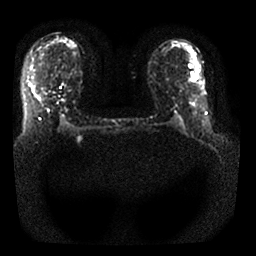
Breast MRI, one axial slice; slice 12 of 25 in the series (ordered by position); diffusion-weighted series; image 2 of 4 stored at this slice position (different b-values; order by instance number); 1.5 T; 4 mm slice thickness; 256 × 256 image matrix. Female patient.
Annotated regions visible in this slice (outlined manually by an expert reader):
- tumour on diffusion-weighted imaging: bounding box [x1, y1, x2, y2] px = [192, 78, 204, 86]